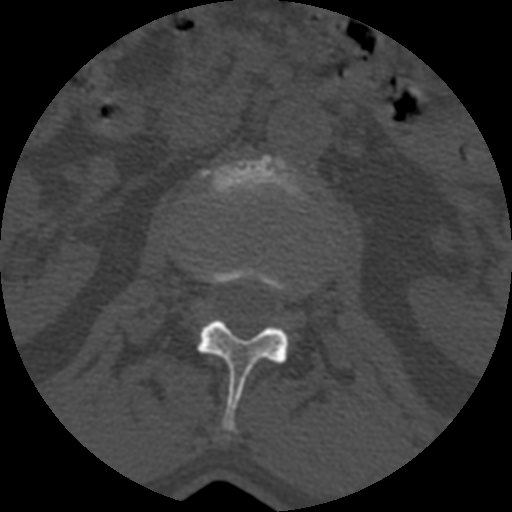
CT including the spine, one axial slice; slice 352 of 399 in the series (ordered by position); reconstruction kernel STANDARD; 120 kVp; bone window (W 1800 / L 400 HU); 1.25 mm slice thickness; 512 × 512 image matrix, field of view 160 × 160 mm. Patient age 71 years. Case-level facts recorded for this patient, not image findings: primary cancer: prostate.
Structures marked on this image (semi-automatically segmented with operator editing):
- L1 vertebra: bounding box <191,264,291,436> (left, top, right, bottom; pixels)
- L2 vertebra: <206,154,302,202>